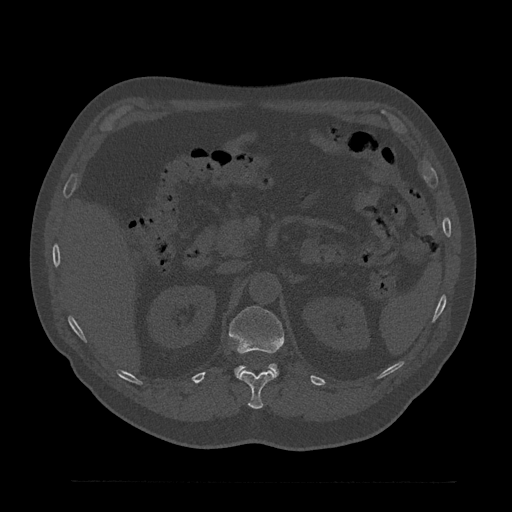
CT including the spine, one axial slice; position 199 of 797 along the scan axis; 120 kVp; bone window (W 1800 / L 400 HU); 0.5 mm slice thickness; 512 × 512 image matrix, field of view 430 × 430 mm. Male patient, age 61 years. From the clinical record (not read from this slice): primary cancer: prostate.
Structures marked on this image (semi-automatically segmented with operator editing):
- L1 vertebra: bounding box (x1, y1, x2, y2) in pixels: (229, 306, 284, 377)
- T12 vertebra: (238, 371, 275, 409)